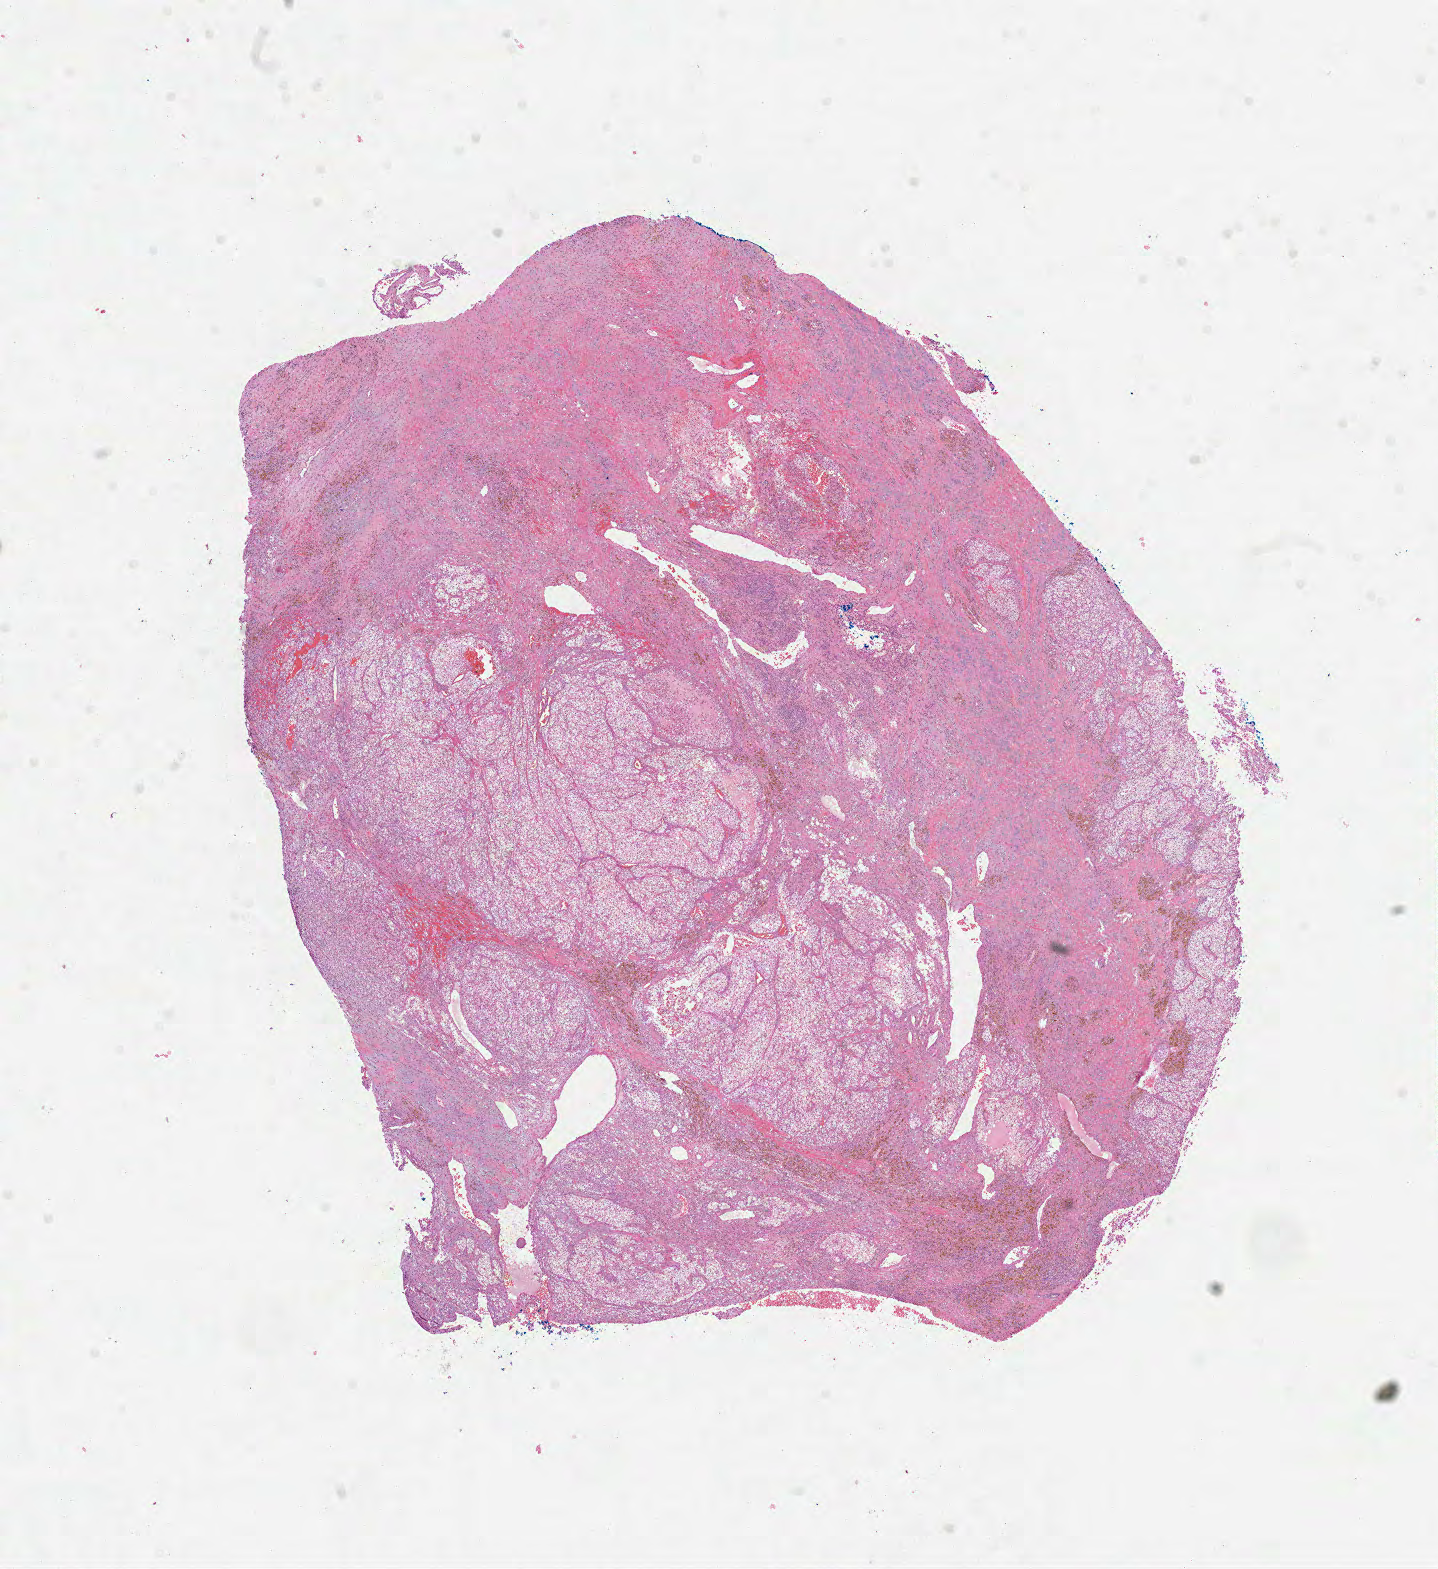
H&E-stained whole-slide image — shown as a low-resolution overview of the whole scanned area (about 11.6 x 12.7 mm, from a 40x scan); formalin-fixed paraffin-embedded (FFPE) diagnostic section; kidney, primary tumour sample. Male patient; age at initial diagnosis 49 years. Histologic grade: G2 (moderately differentiated).
• diagnosis: Clear cell adenocarcinoma, NOS
• AJCC pathologic stage: I